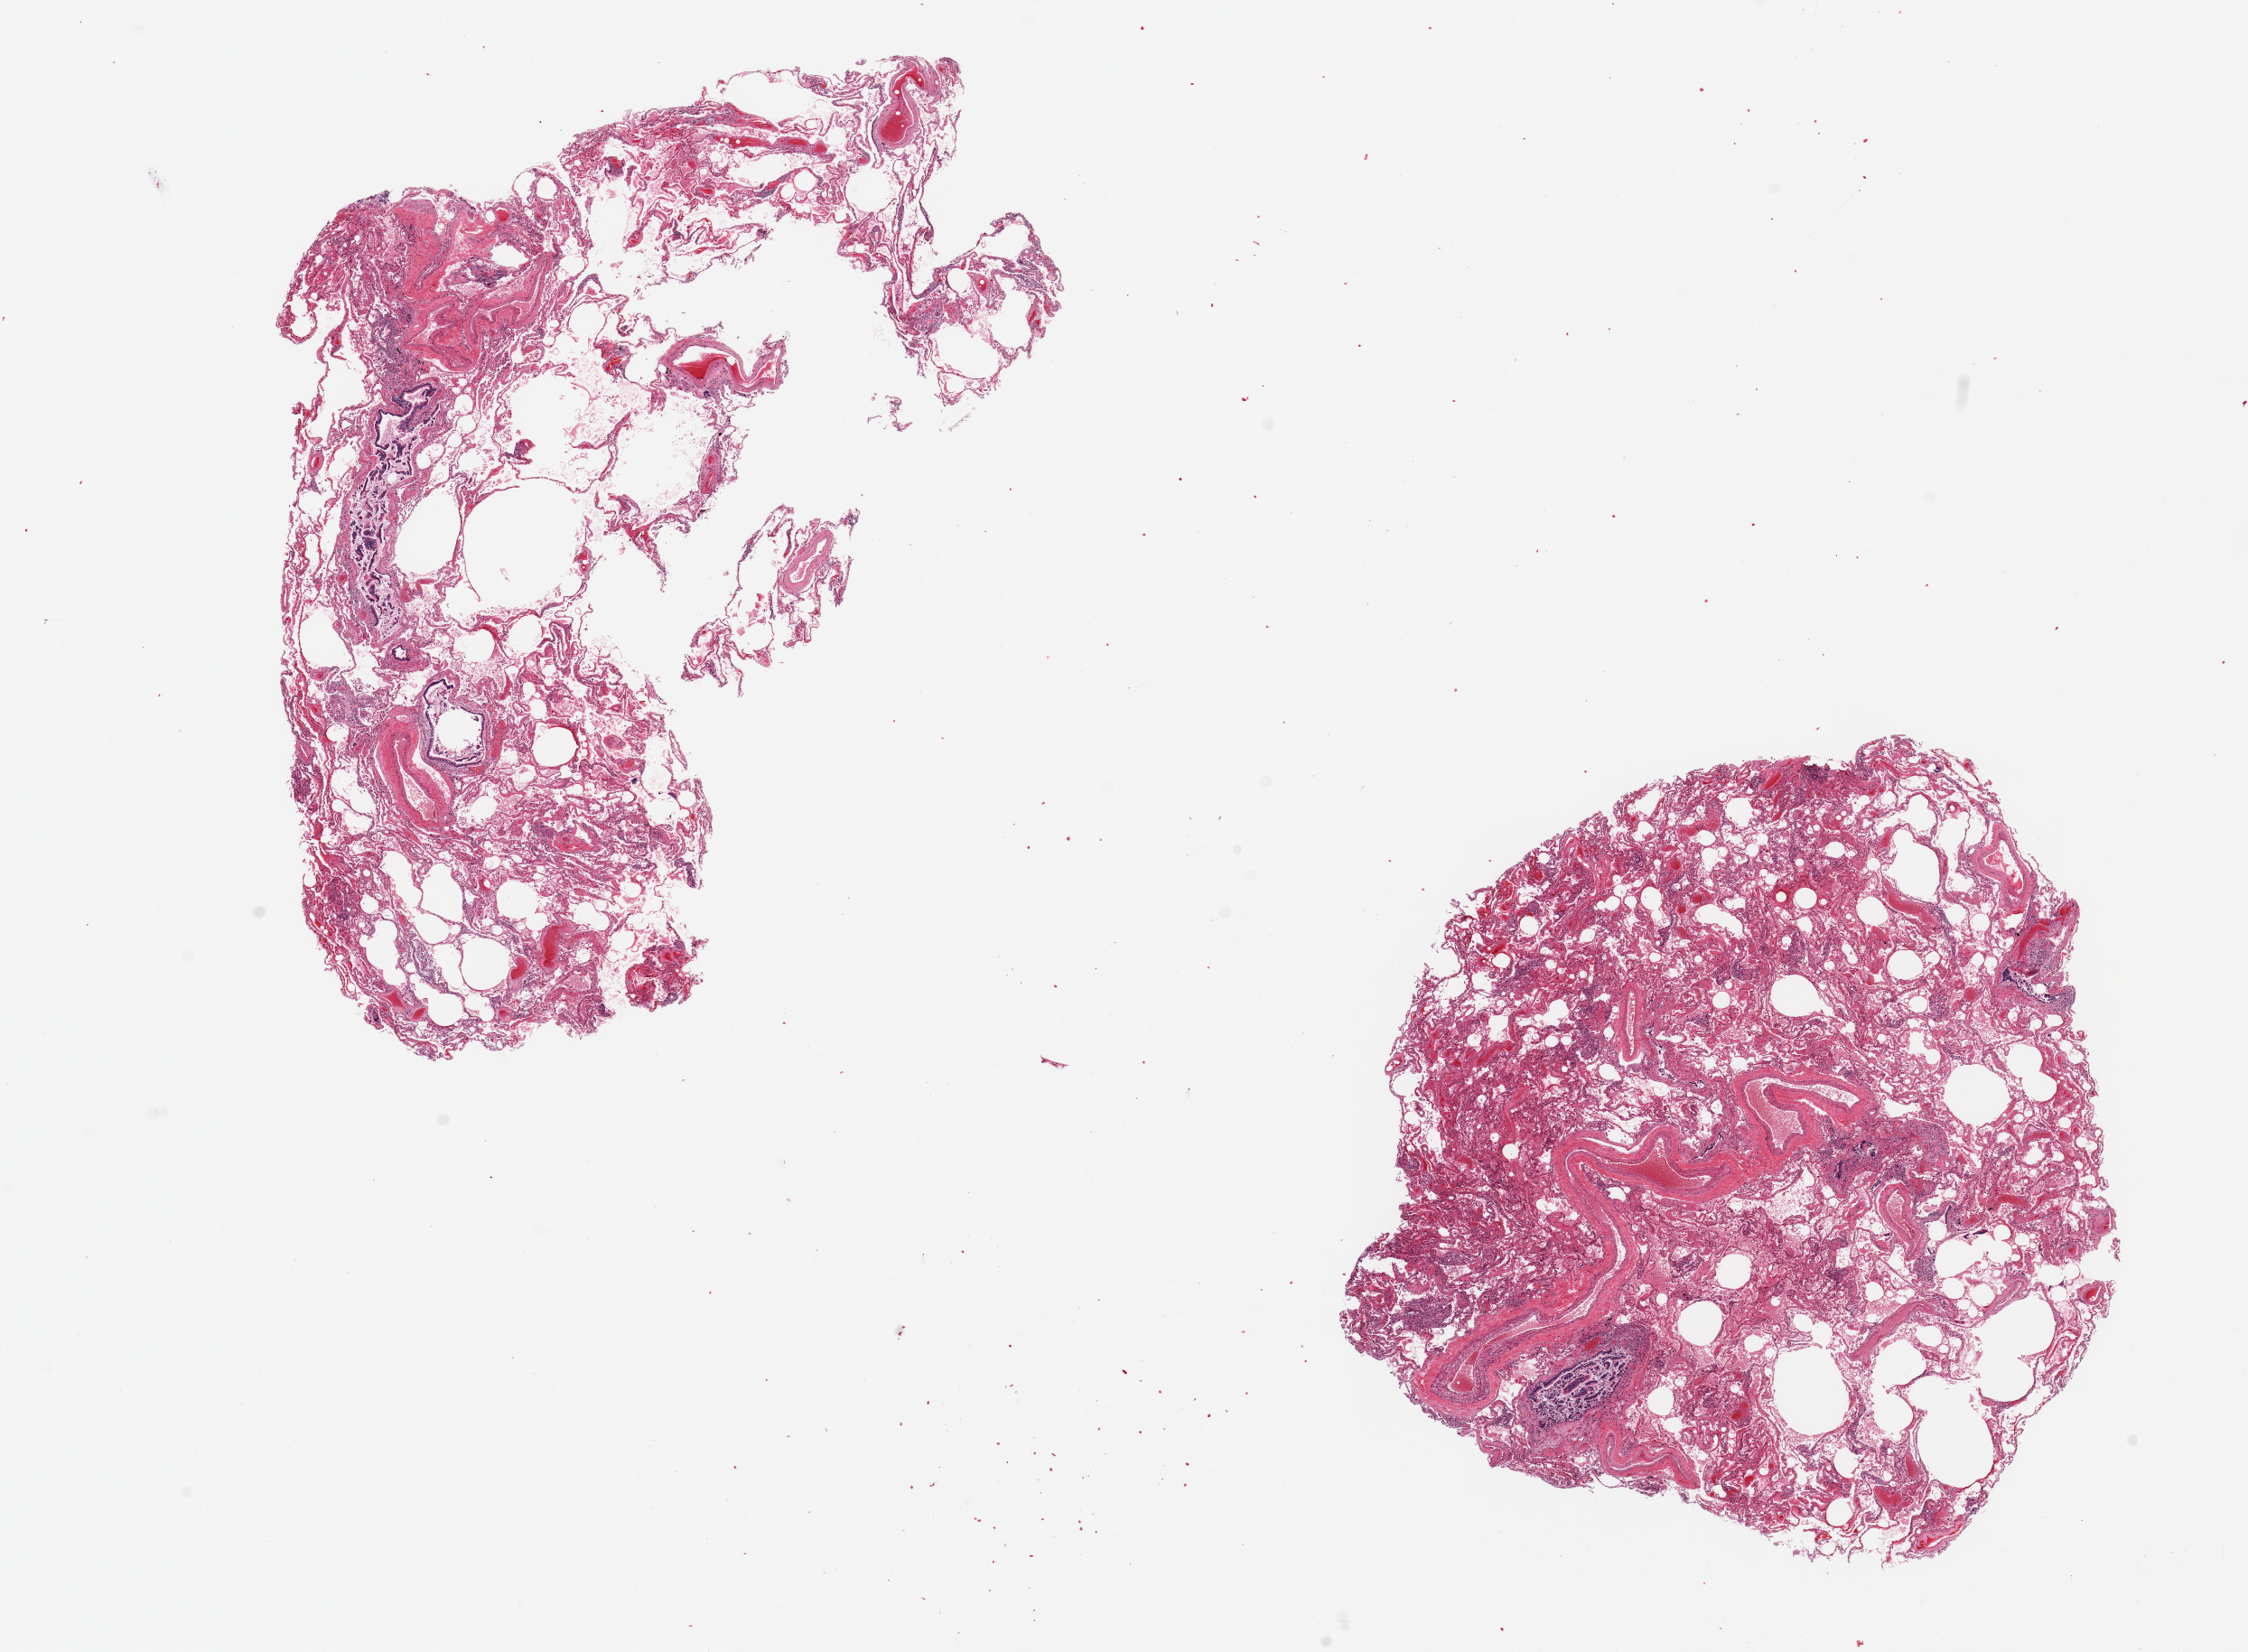
H&E whole-slide image, low-resolution overview of the scanned area, about 19.7 x 14.5 mm (from a 20x scan); PAXgene-fixed paraffin-embedded (PFPE) section; target tissue: lung; donor tissue sample. Donor: female.
Review note (as recorded): 2 pieces, 10x6 & 7x7mm; emphysematous changes; giant cells c/w aspiration.